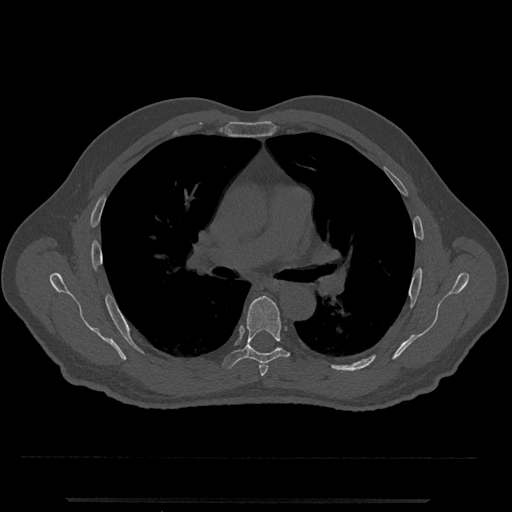
CT including the spine, one axial slice. Slice 744 of 797 in the series (ordered by position). Reconstruction kernel Br40s/3. Bone window (W 1800 / L 400 HU). 0.5 mm slice thickness. 512 × 512 image matrix, field of view 419 × 419 mm. Patient: male, 63 years. Case-level facts recorded for this patient, not image findings: primary cancer: prostate.
Annotated regions visible in this slice (semi-automatic segmentation, software-assisted and operator-edited):
- T5 vertebra: bounding box (x1, y1, x2, y2) in pixels: (259, 363, 268, 376)
- T6 vertebra: (222, 296, 289, 369)